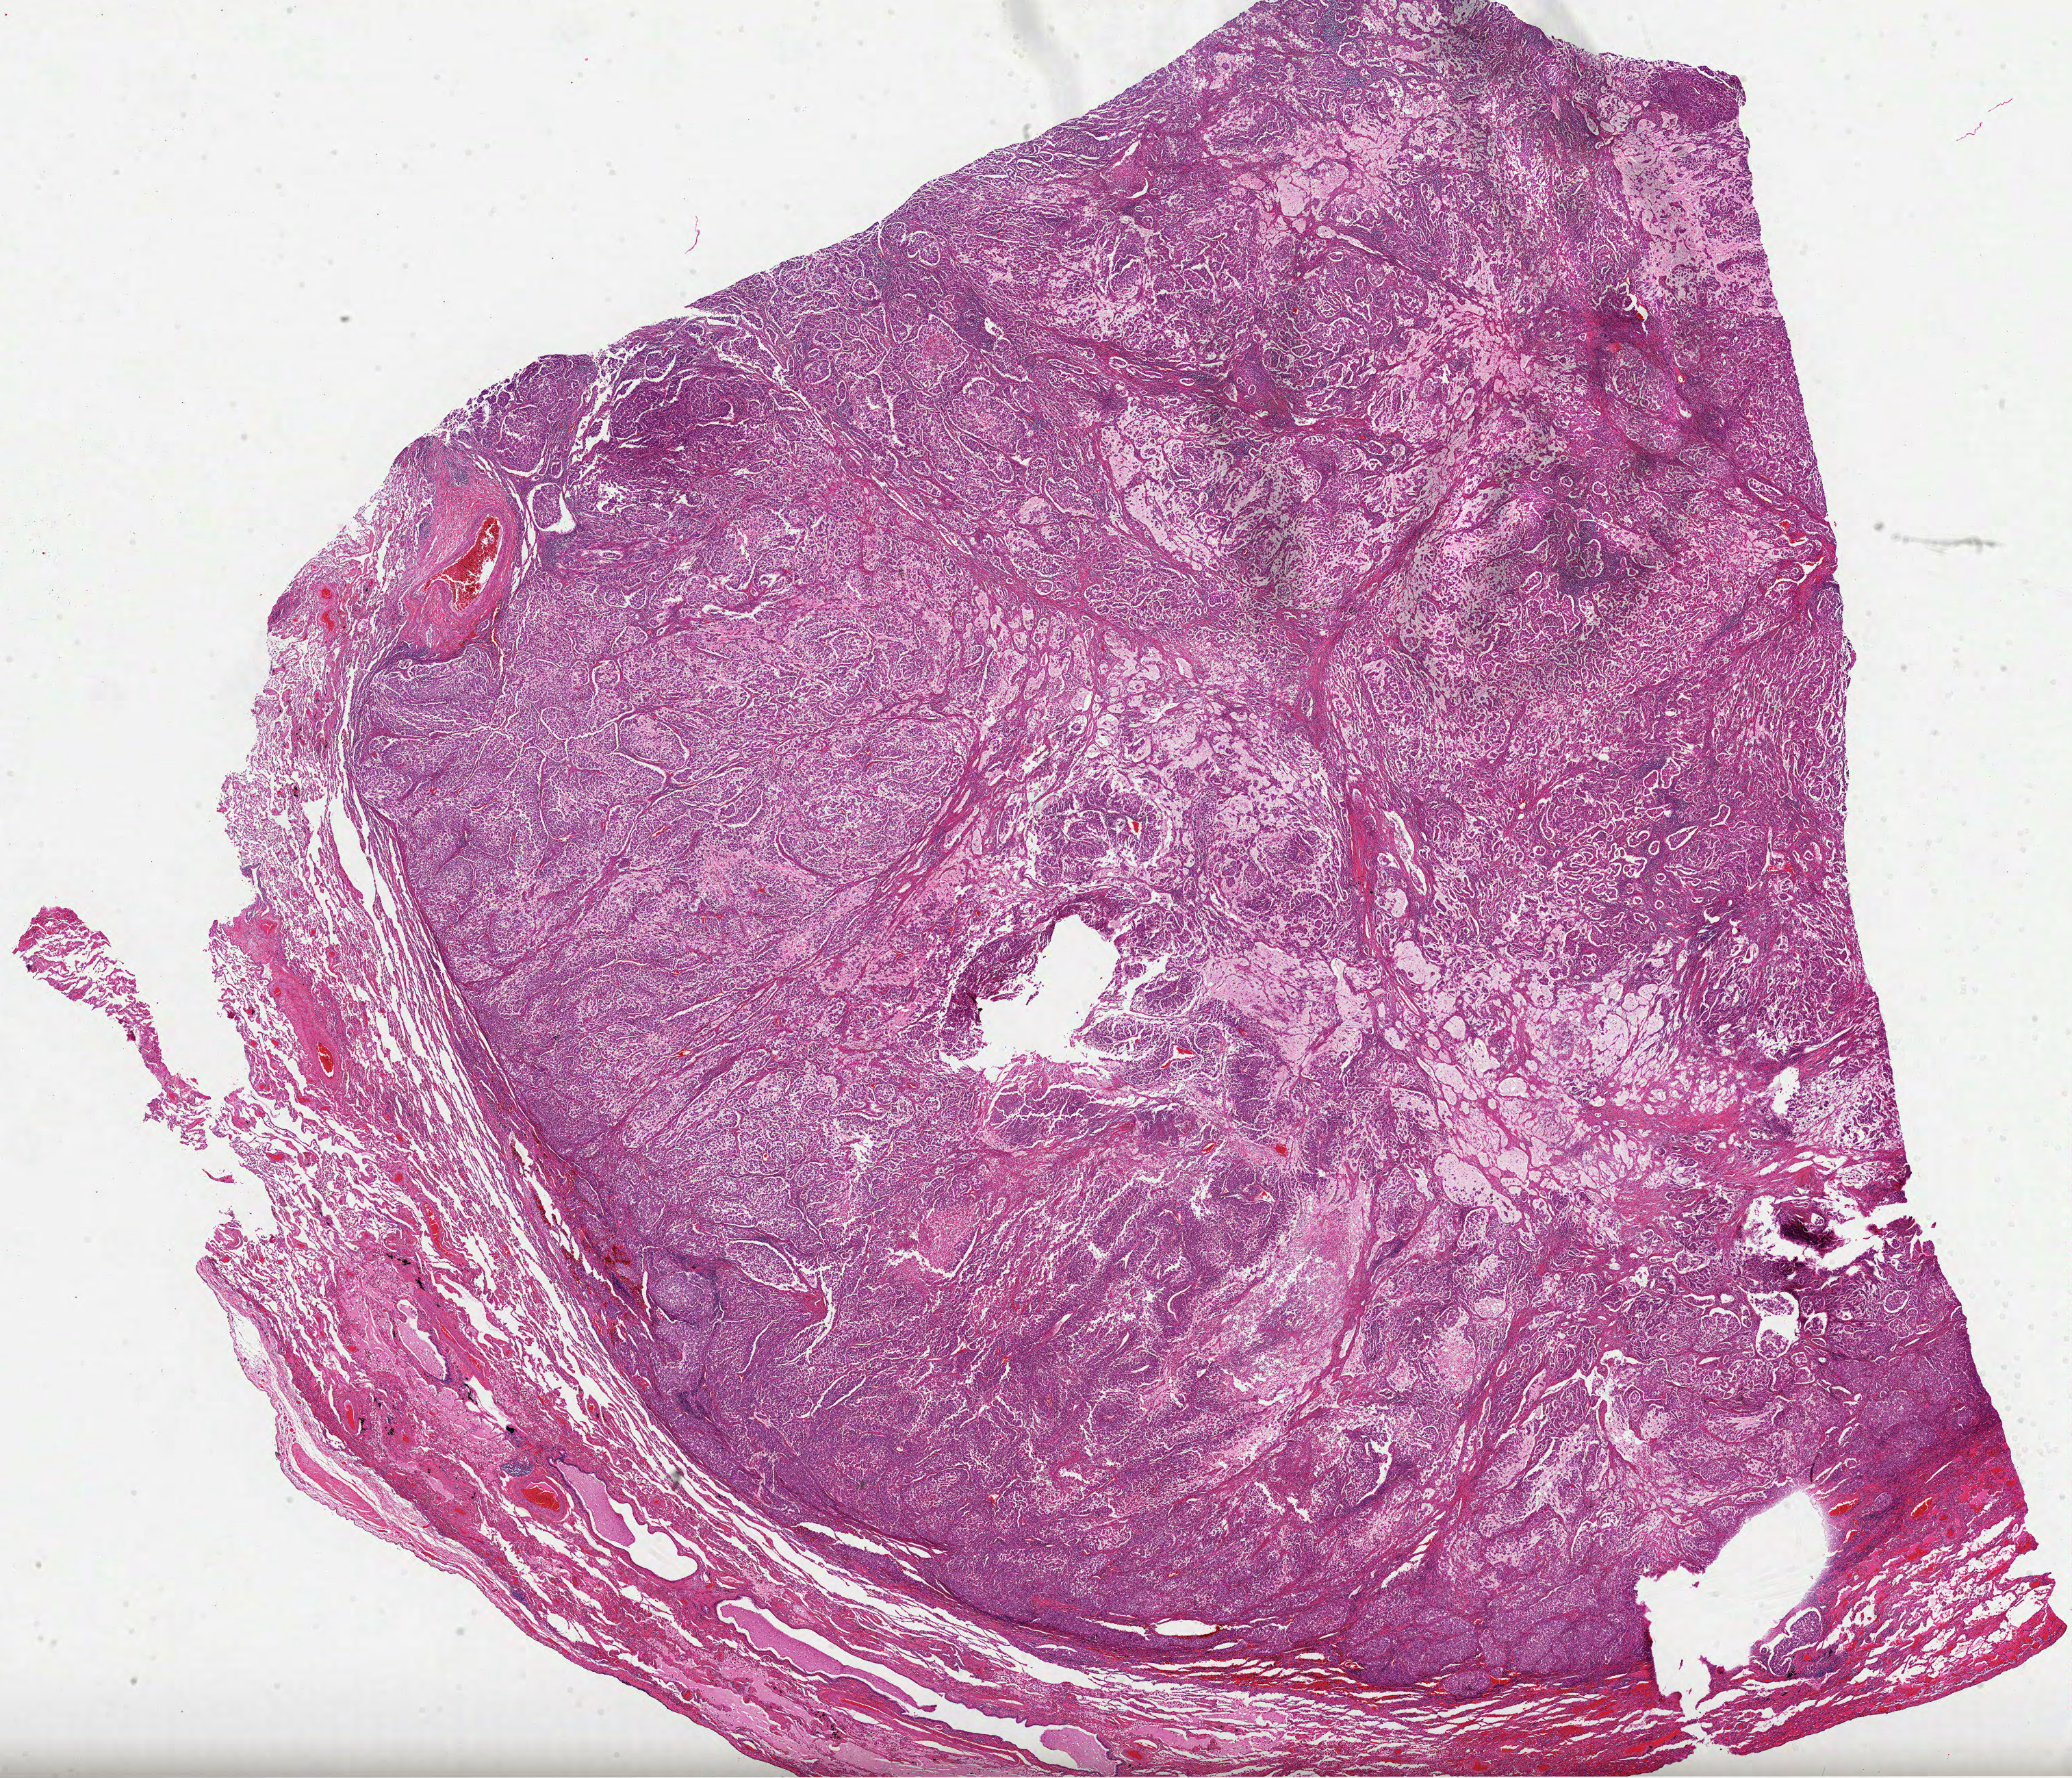
Whole-slide histology image, H&E-stained, whole scanned area (about 24.4 x 20.9 mm) shown as a low-resolution overview. Formalin-fixed paraffin-embedded (FFPE) diagnostic section. Primary tumour sample from the lung. Patient: female, age at initial diagnosis 68 years.
Pathologic diagnosis: Adenocarcinoma, NOS (upper lobe, lung). AJCC pathologic stage: IIB (4th edition).